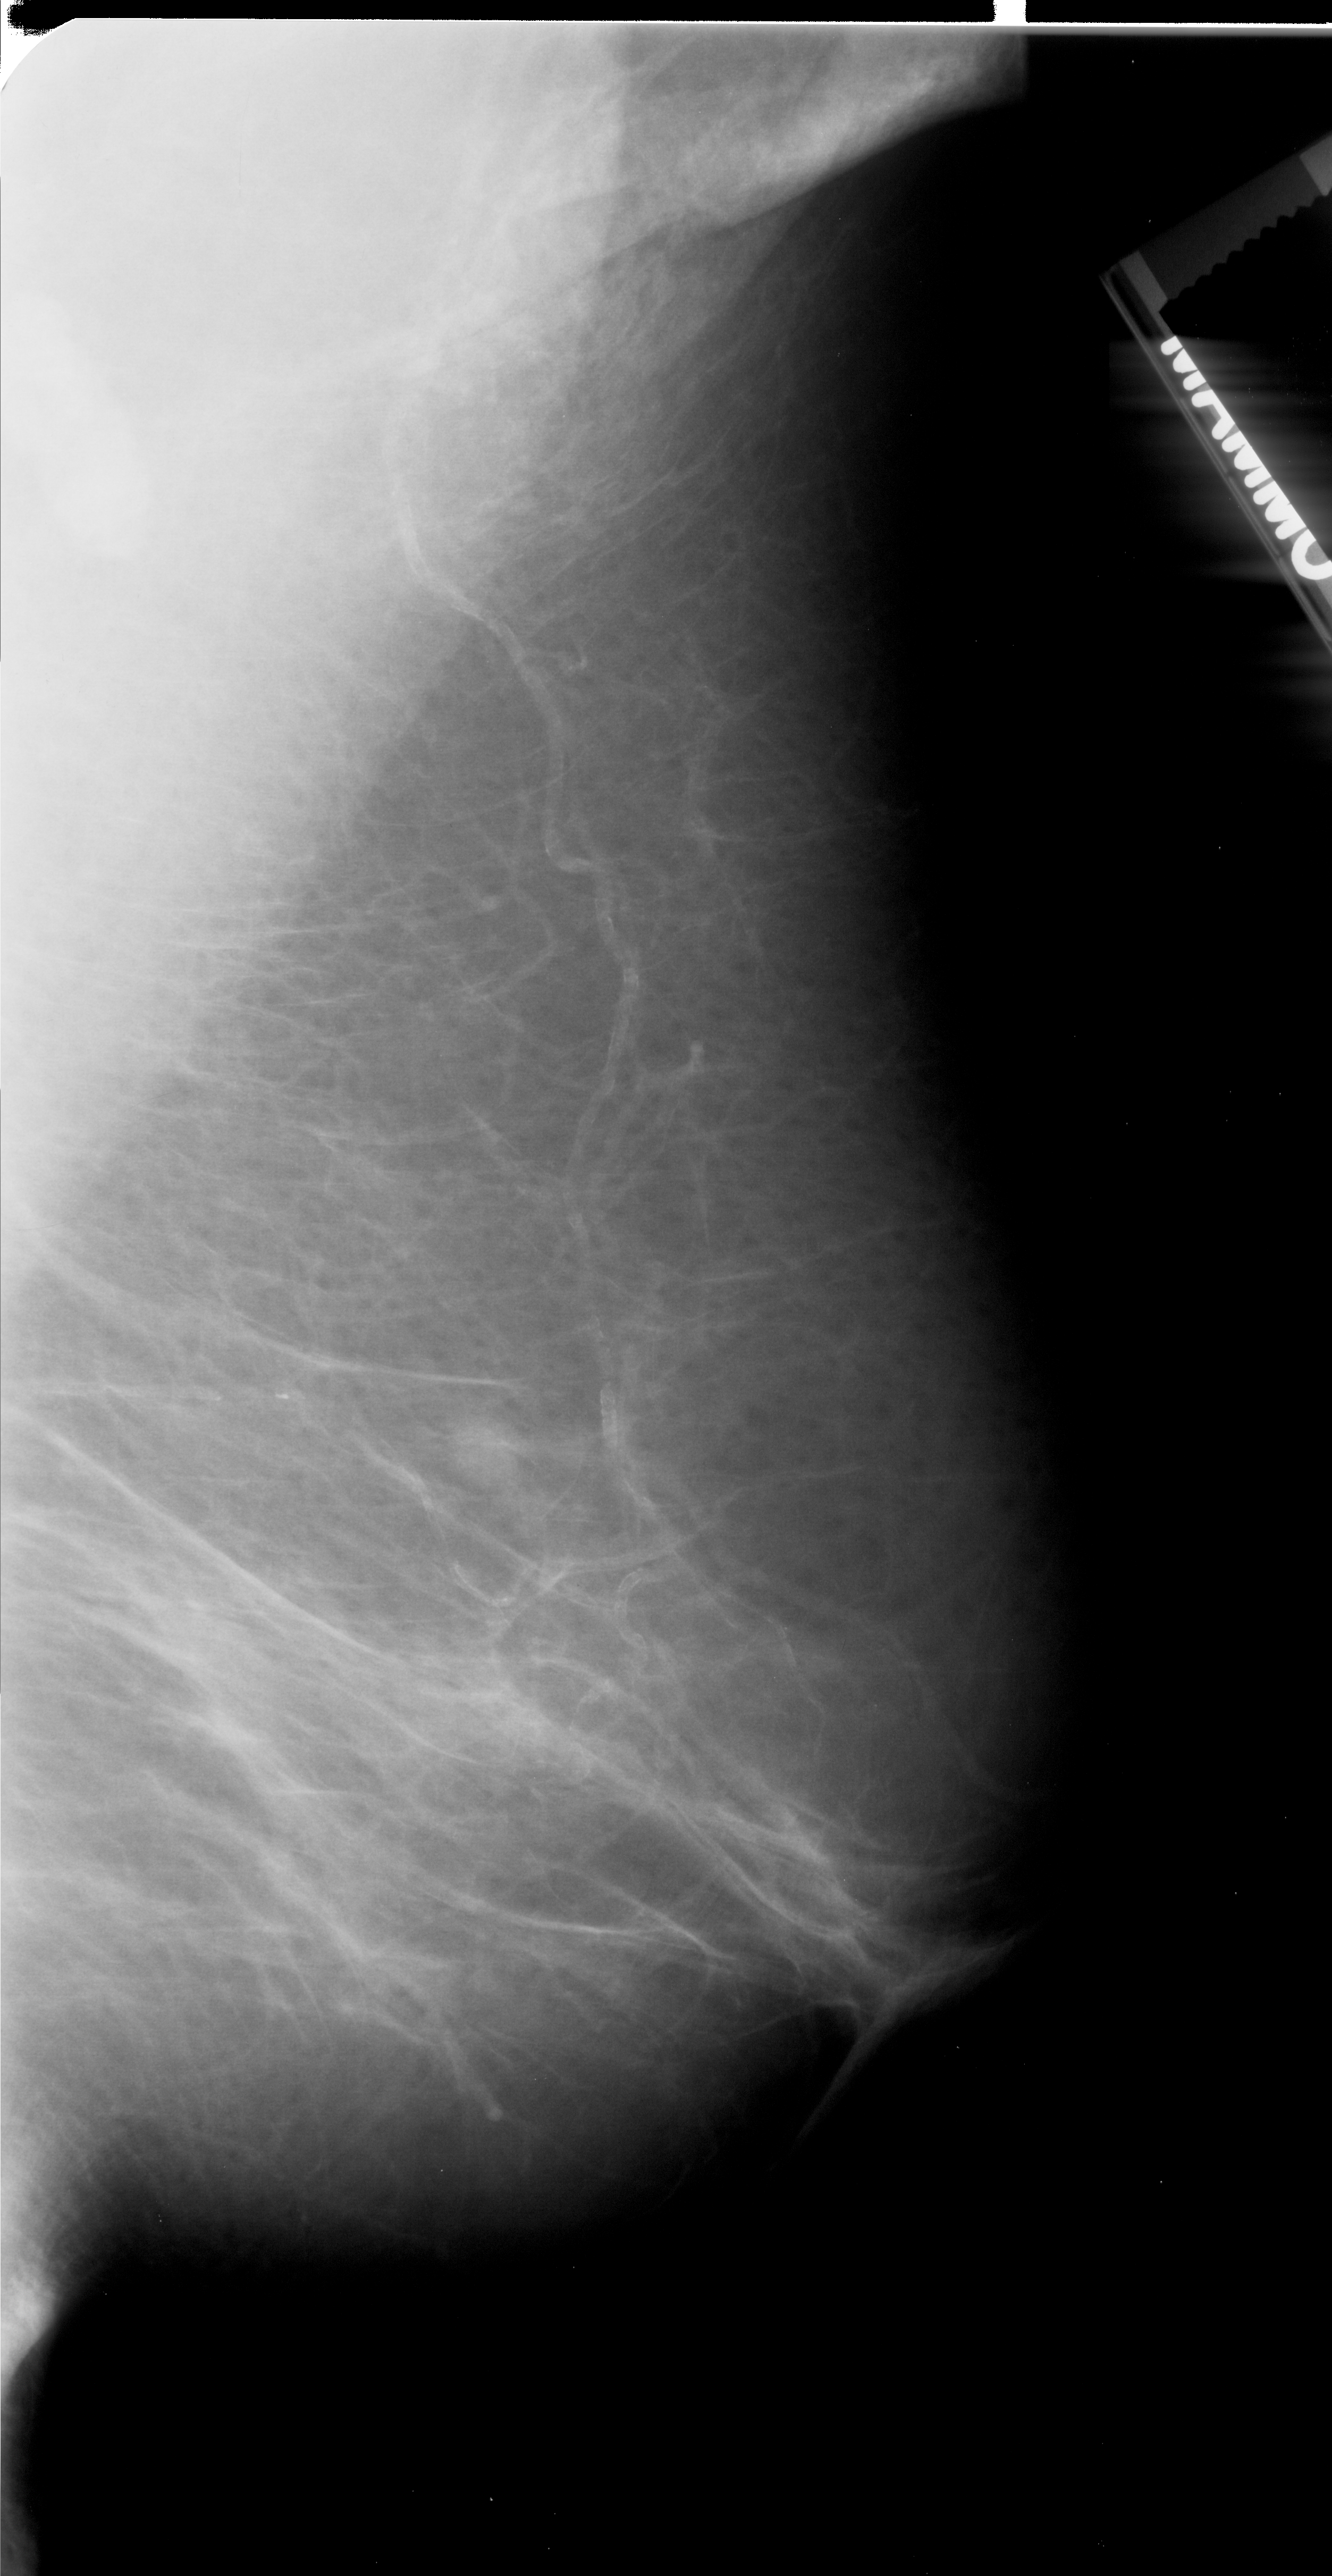
Digitized screen-film mammogram; right breast; MLO view; breast composition: almost entirely fatty (BI-RADS density category 1 of 4); 1332 × 2576 image matrix.
Expert-marked regions of interest on this film, with their recorded descriptors:
- mass, shape irregular, margins ill defined; BI-RADS assessment category 4; subtlety rating 5 on a 1 (subtle) to 5 (obvious) scale; pathology result (as recorded, not read from the image): malignant: bounding box (x1, y1, x2, y2) in pixels: (443, 1404, 546, 1497)